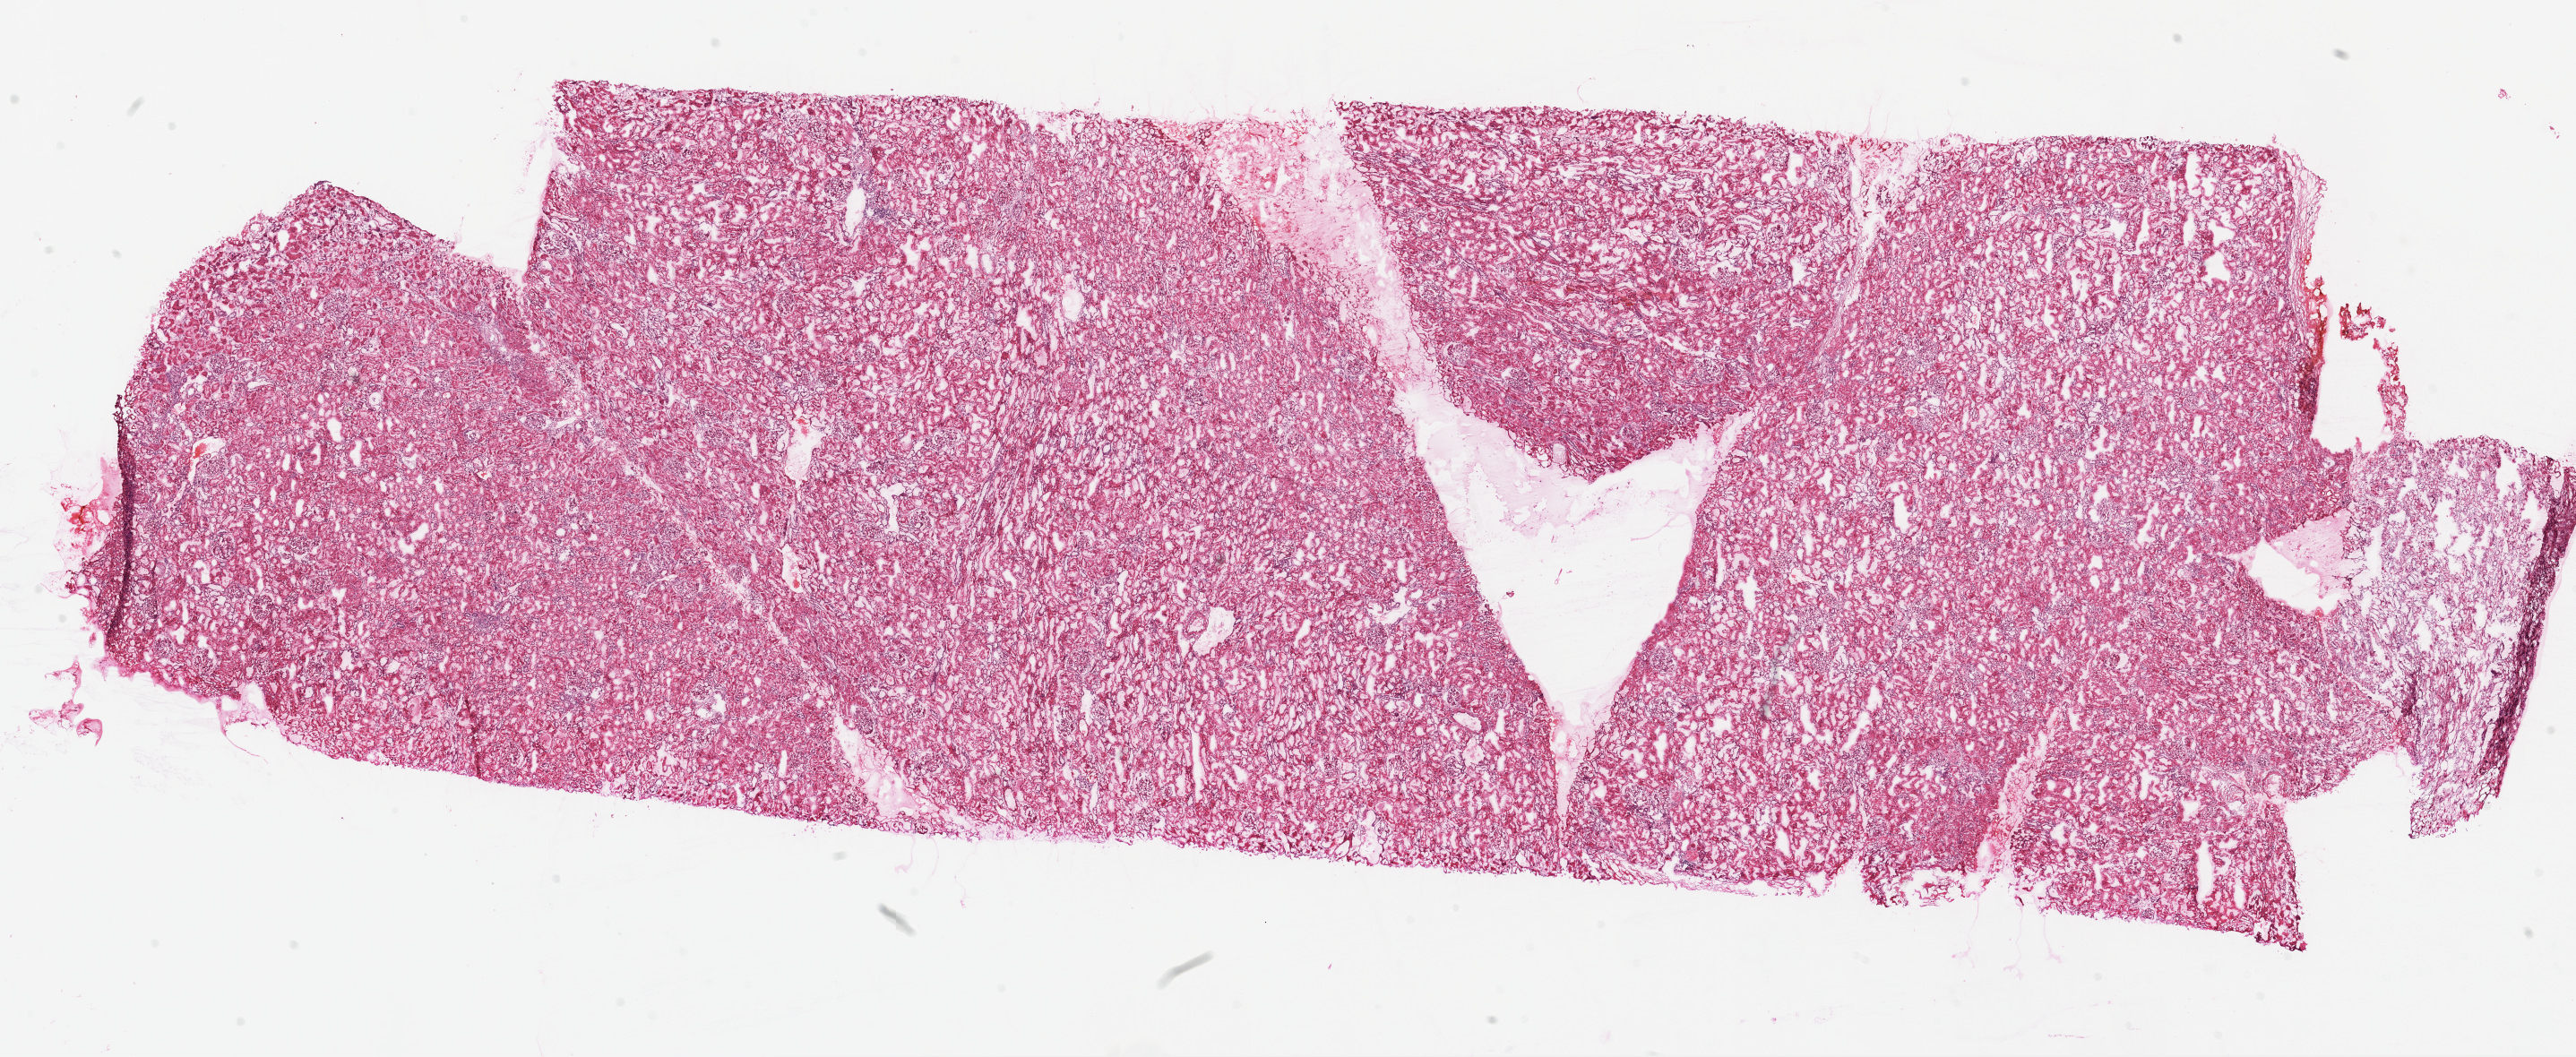
Whole-slide histology image, H&E-stained, a low-resolution overview of the entire scanned area, about 23.1 x 9.5 mm, frozen section from the top of the tissue portion, kidney, solid tissue normal (non-tumour tissue) sample. Female, age 55 years at initial diagnosis.
This section: solid tissue normal (non-tumour) sample from the same patient. Patient diagnosis: Clear cell adenocarcinoma, NOS.